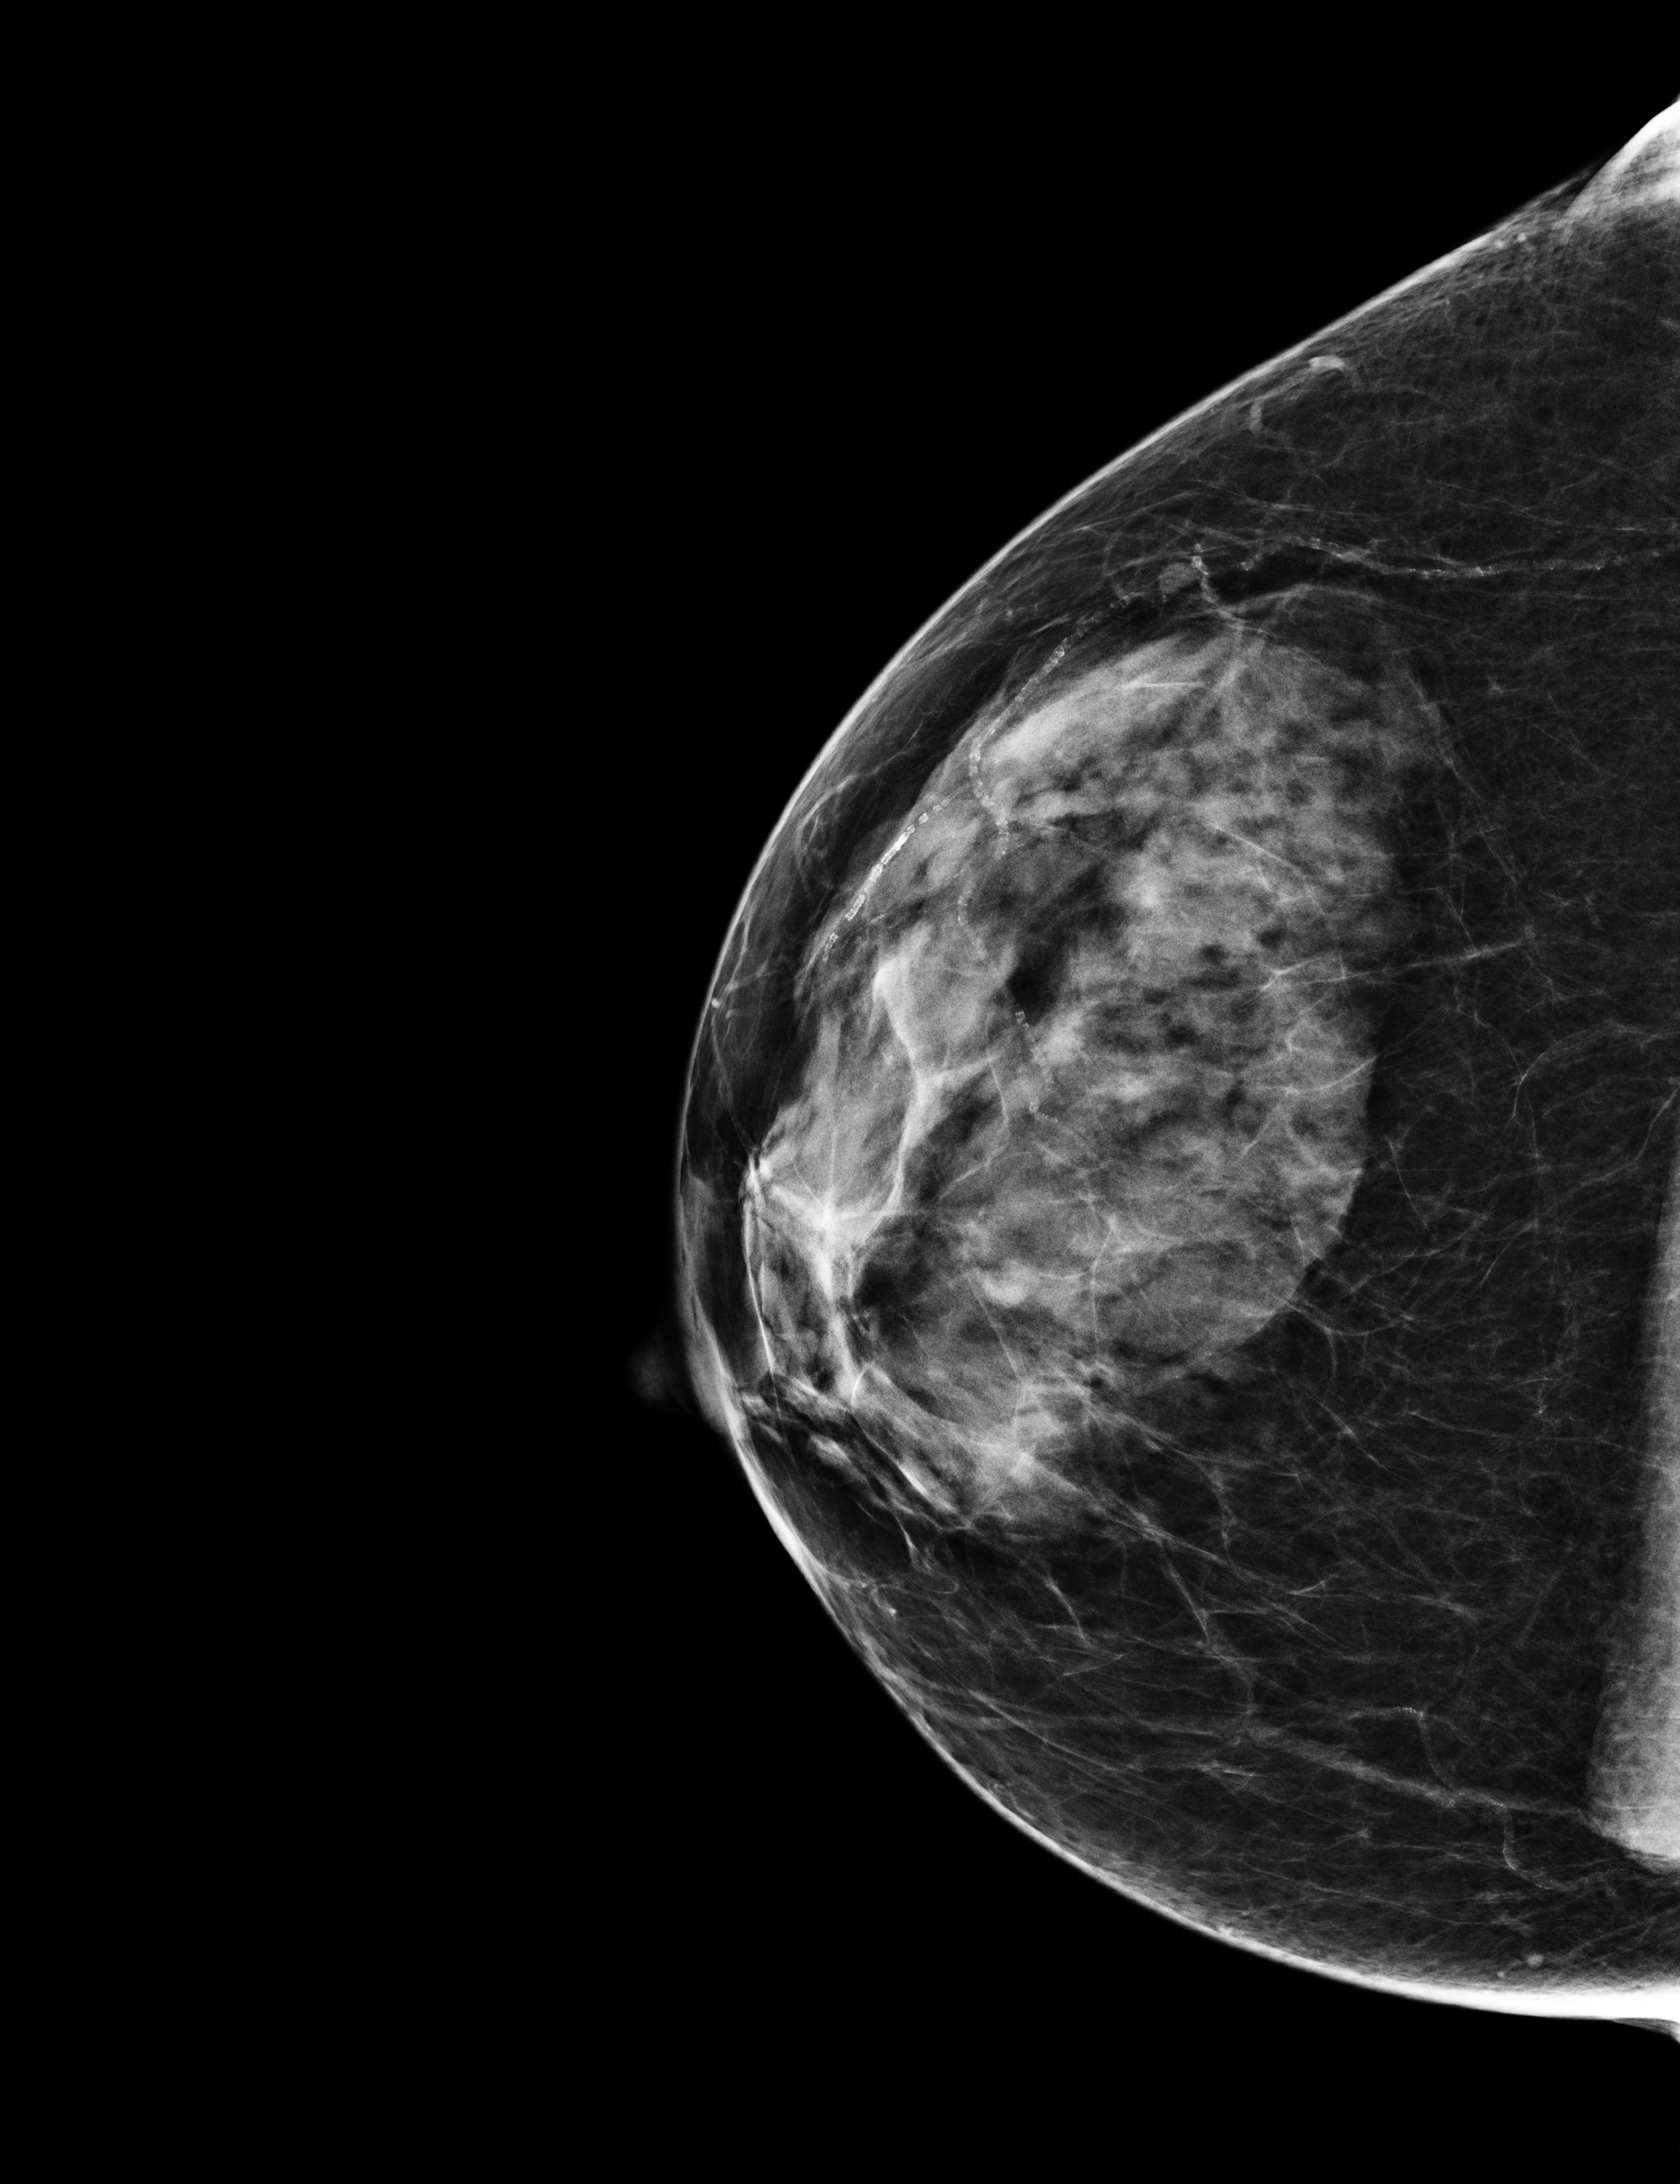
Screening examination; system: Selenia Dimensions. Patient aged 58 years (female).
Image type: full-field digital mammogram. Breast: right. Projection: craniocaudal (CC) view.